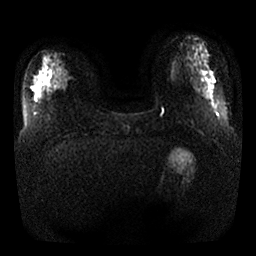
Breast MRI, one axial slice; position 7 of 32 along the scan axis; diffusion-weighted series; image 2 of 4 stored at this slice position (different b-values; order by instance number); 1.5 T; 4 mm slice thickness; 256 × 256 image matrix, field of view 350 × 350 mm. Female patient.
Structures marked on this image (manually delineated by an expert):
- tumour on diffusion-weighted imaging: box from (x=55, y=76) to (x=67, y=88) px